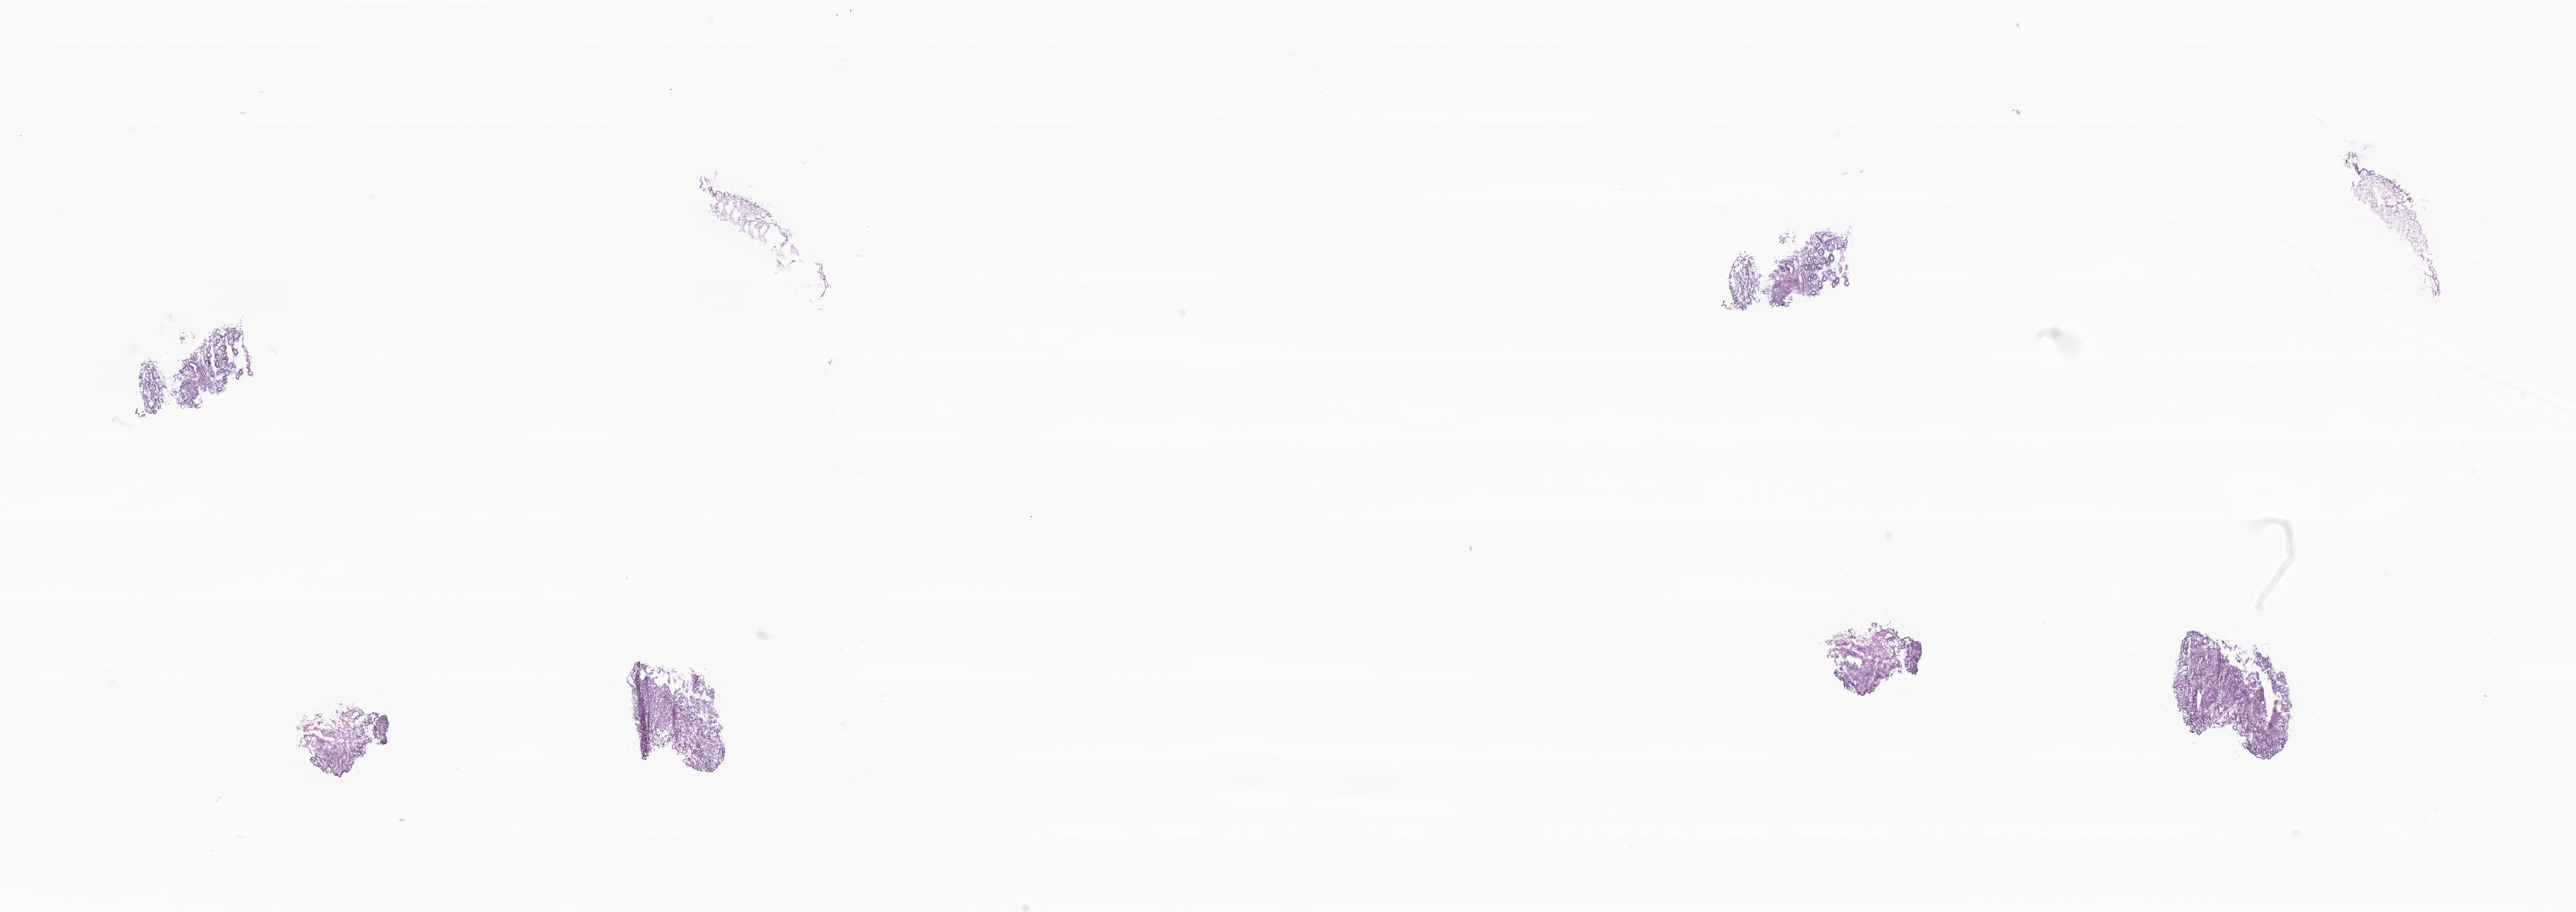
Hematoxylin and eosin (H&E) whole-slide image, shown as a low-resolution overview of the whole scanned area (about 34.7 x 12.3 mm), frozen section, specimen: primary tumor, anatomic site: cecum. Female patient; age at initial diagnosis 82 years. Slide review estimates, as recorded: tumor cells 44%, tumor nuclei 72%, stromal cells 45%, necrosis 2%, normal cells 9%. Inflammatory infiltration, as recorded: lymphocyte infiltration 18%, monocyte infiltration 2%, neutrophil infiltration 0%.
* diagnosis: Adenocarcinoma, NOS
* section: bottom of the tissue portion